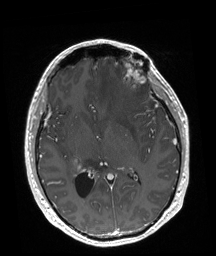
Brain MRI from a brain-tumour surgery series, one axial slice; slice 94 of 192 in the series (ordered by position); T1-weighted post-contrast; 216 × 256 image matrix, field of view 219 × 260 mm. Case-level facts recorded for this patient, not image findings: tumour location: Left Frontal.
Outlined on this slice (manually delineated by an expert):
- tumour: bounding box <122,57,145,90> (left, top, right, bottom; pixels)